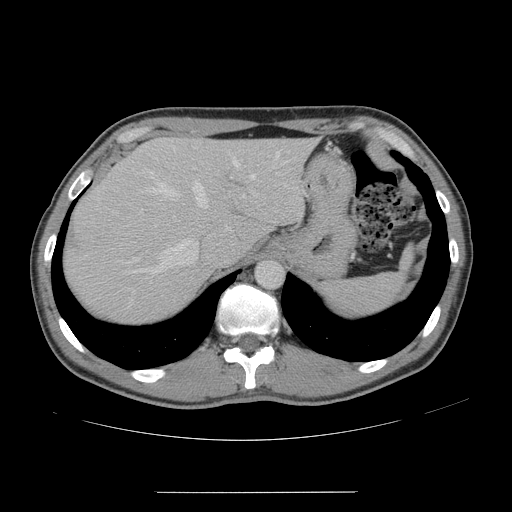
Contrast-enhanced abdominal CT, one axial slice. Position 118 of 178 along the scan axis. 120 kVp. Intravenous contrast given. Soft-tissue window (W 400 / L 40 HU). 512 × 512 image matrix, field of view 401 × 401 mm. Male patient, age 53 years. Case-level facts recorded for this patient, not image findings: diagnosis: colorectal cancer liver metastases, imaged before liver resection; multiple liver metastases: yes.
Outlined on this slice (outlined manually by an expert reader):
- hepatic veins: box from (x=135, y=151) to (x=279, y=274) px
- liver: (x=65, y=138)–(x=313, y=322)
- planned liver remnant (the part of the liver to remain after resection): (x=148, y=139)–(x=313, y=246)
- portal vein (with intrahepatic branches): (x=139, y=193)–(x=257, y=214)